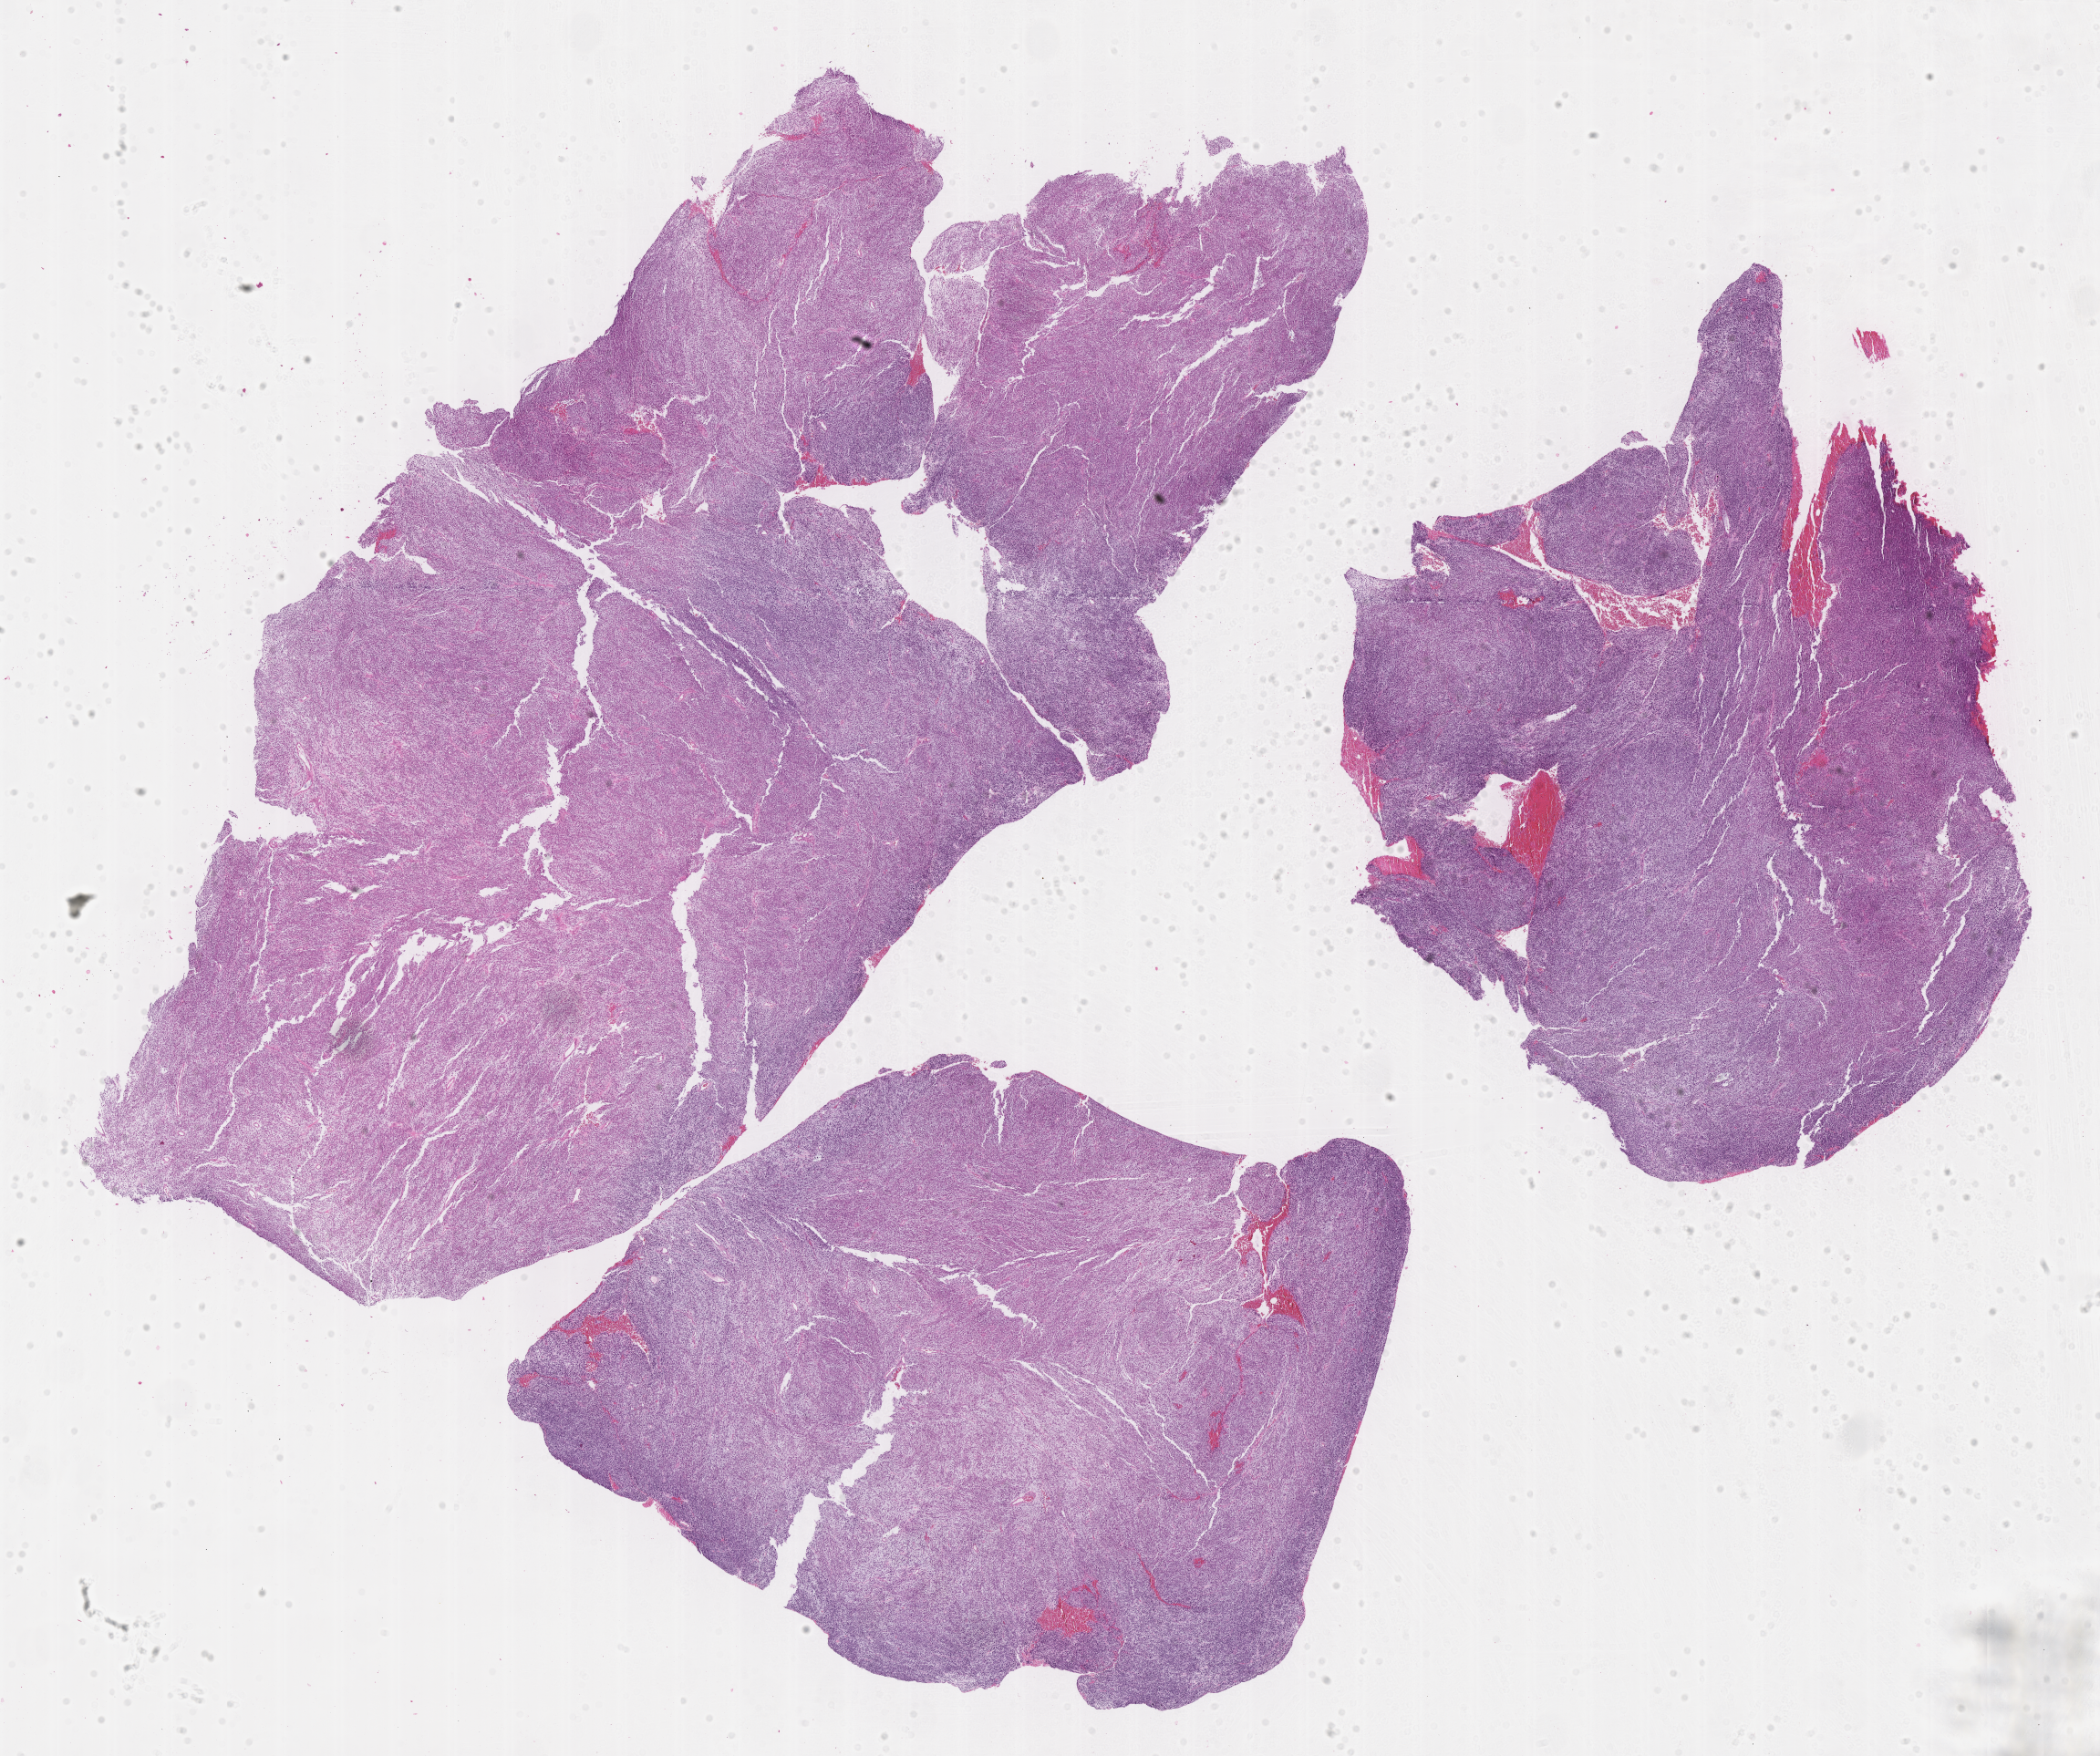
Whole-slide image, H&E stain of tumor tissue, shown as a low-resolution overview of the whole scanned area (about 18.6 x 15.6 mm); formalin-fixed, paraffin-embedded (FFPE) tissue; sample anatomic site: eye, orbit-left. Patient: male, age 4.2 years at diagnosis.
Diagnosis: rhabdomyosarcoma; histological classification: embryonal rhabdomyosarcoma.